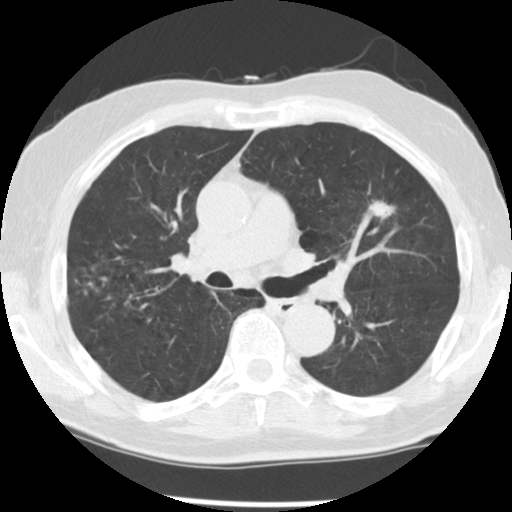
Low-dose screening chest CT, one axial slice; slice 77 of 131 in the series (ordered by position); lung window (W 1500 / L -600 HU); 2.5 mm slice thickness; 512 × 512 image matrix, field of view 330 × 330 mm.
Annotated regions visible in this slice (expert manual segmentation):
- lesion 1 (tumor, upper lobe of left lung): bounding box [x1, y1, x2, y2] px = [369, 201, 395, 219]